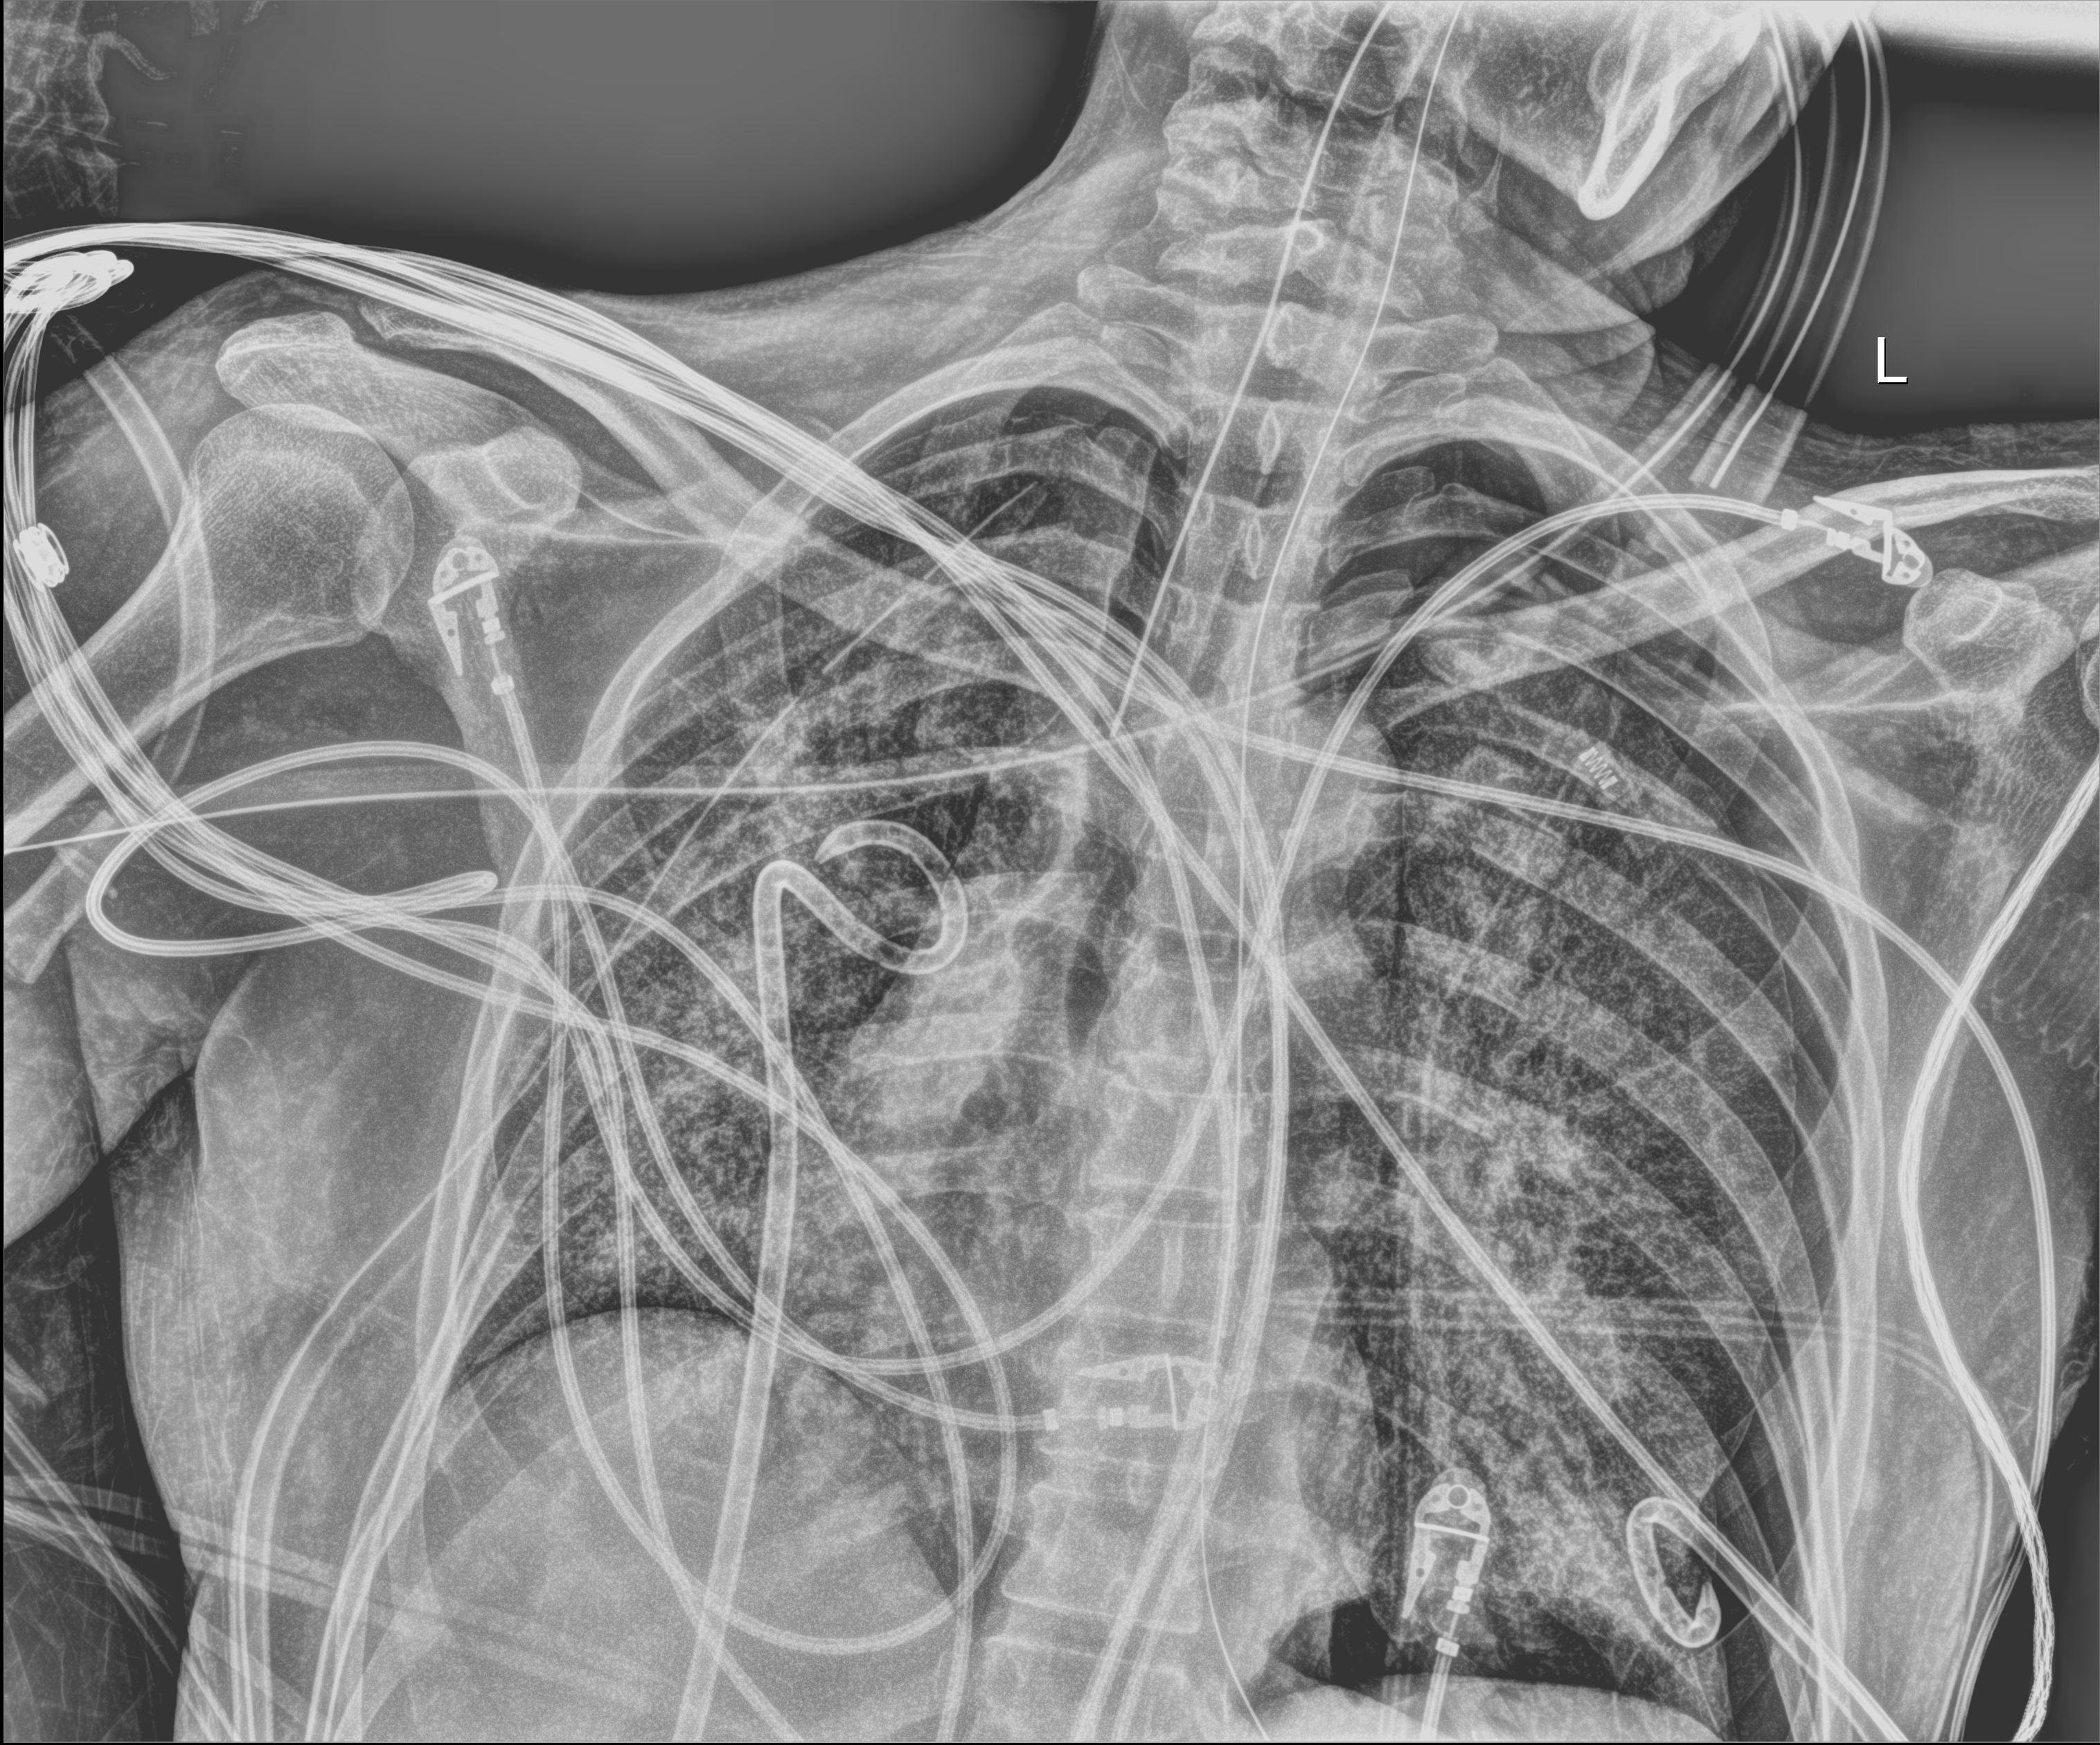
Chest radiograph (digital radiography); anteroposterior (AP) projection. Patient hospitalised with COVID-19, aged 18–59 years.
Hospital-stay facts (about this admission, not read from this image; timing relative to this image not recorded): length of hospital stay: 41 days.